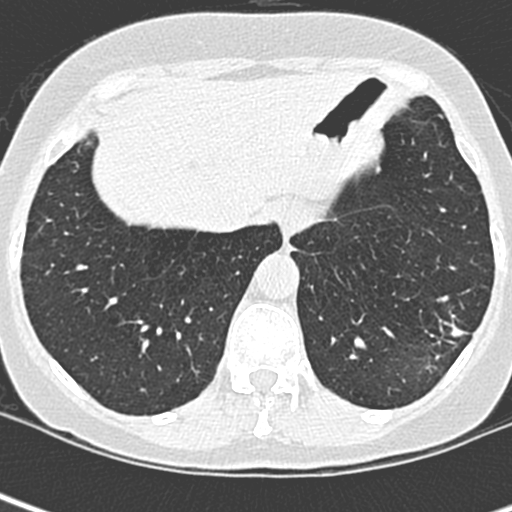
Low-dose screening chest CT, one axial slice; position 66 of 252 along the scan axis; lung window (W 1500 / L -600 HU); 1.3 mm slice thickness; 512 × 512 image matrix, field of view 271 × 271 mm.
Outlined on this slice (outlined manually by an expert reader):
- lesion 1 (tumor, lower lobe of left lung): box from (x=444, y=321) to (x=465, y=337) px